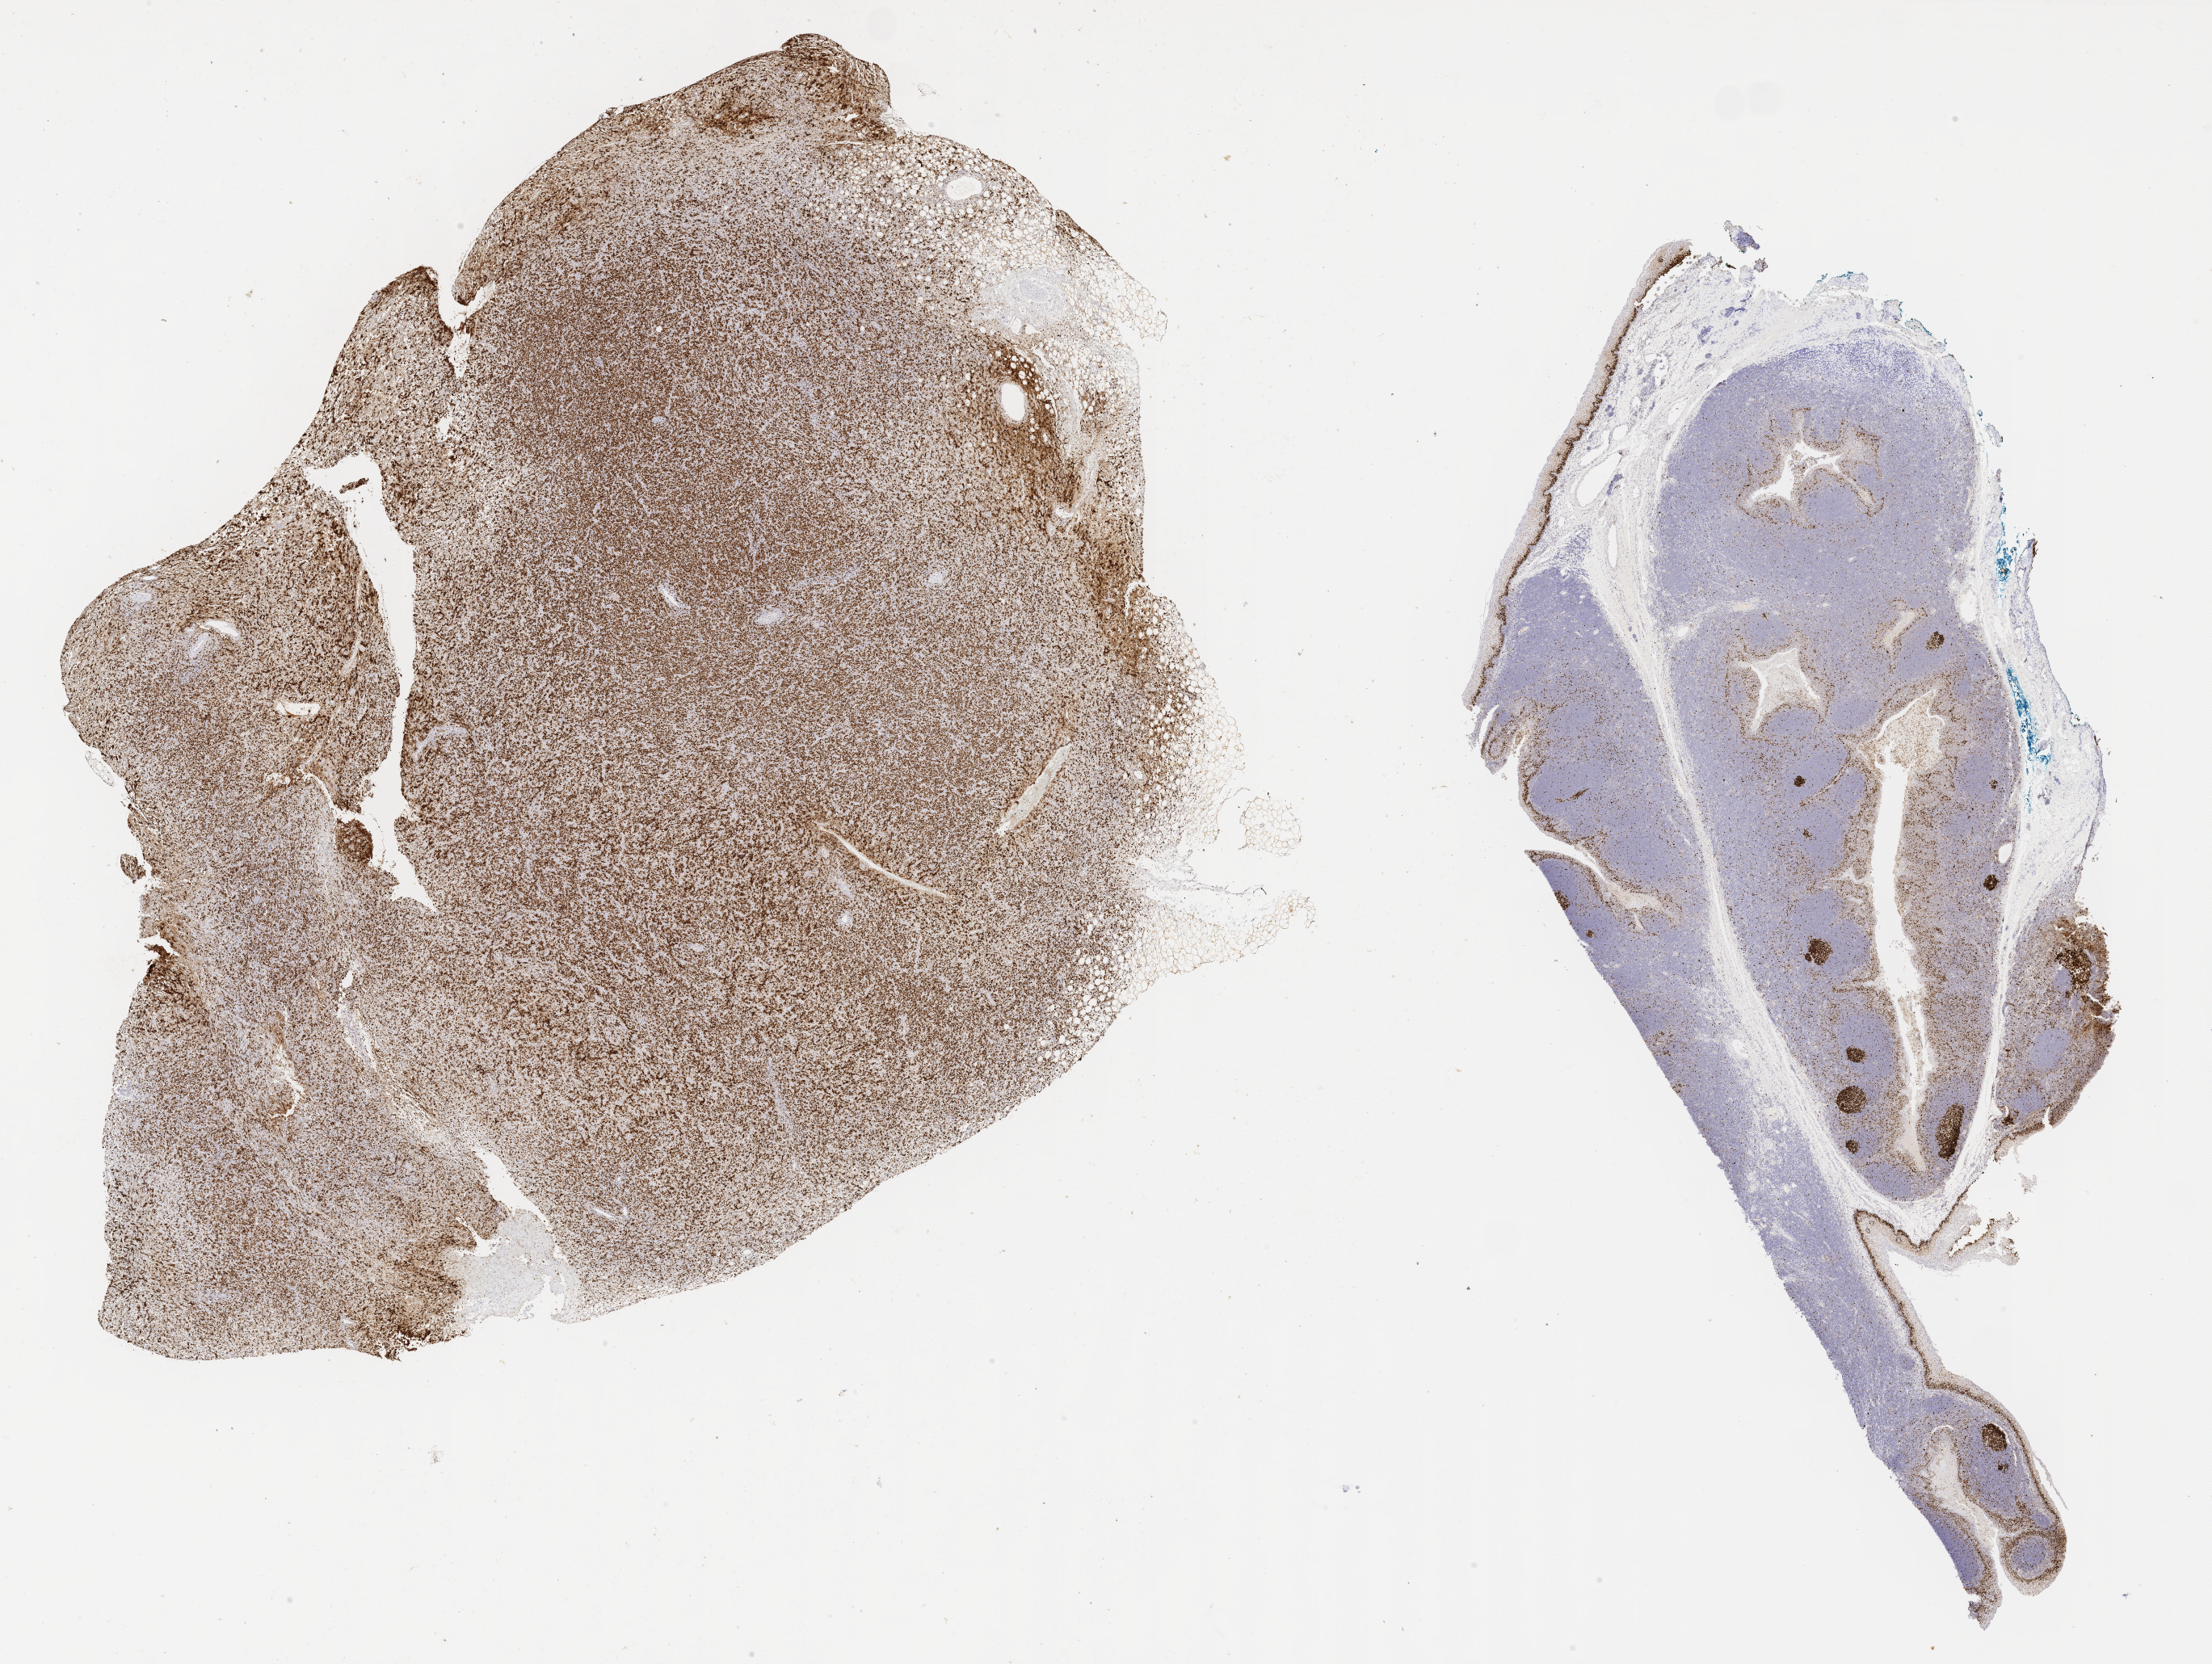
Whole-slide image, immunohistochemical stain for Ki-67, whole scanned area (about 22.1 x 16.7 mm) shown as a low-resolution overview. Patient sex: female.
• specimen: tumor tissue